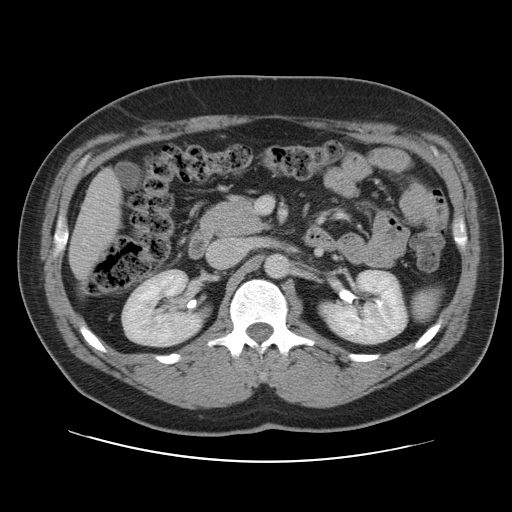
Contrast-enhanced abdominal CT, one axial slice; position 52 of 109 along the scan axis; 120 kVp; intravenous contrast given; soft-tissue window (W 400 / L 40 HU); 5 mm slice thickness; 512 × 512 image matrix, field of view 402 × 402 mm. Male patient, age 35 years. From the clinical record (not read from this slice): diagnosis: colorectal cancer liver metastases, imaged before liver resection; multiple liver metastases: yes; largest metastasis: 2.8 cm; chemotherapy before resection: yes.
Annotated regions visible in this slice (outlined manually by an expert reader):
- liver: bounding box [x1, y1, x2, y2] px = [70, 172, 120, 279]
- planned liver remnant (the part of the liver to remain after resection): [70, 172, 120, 279]